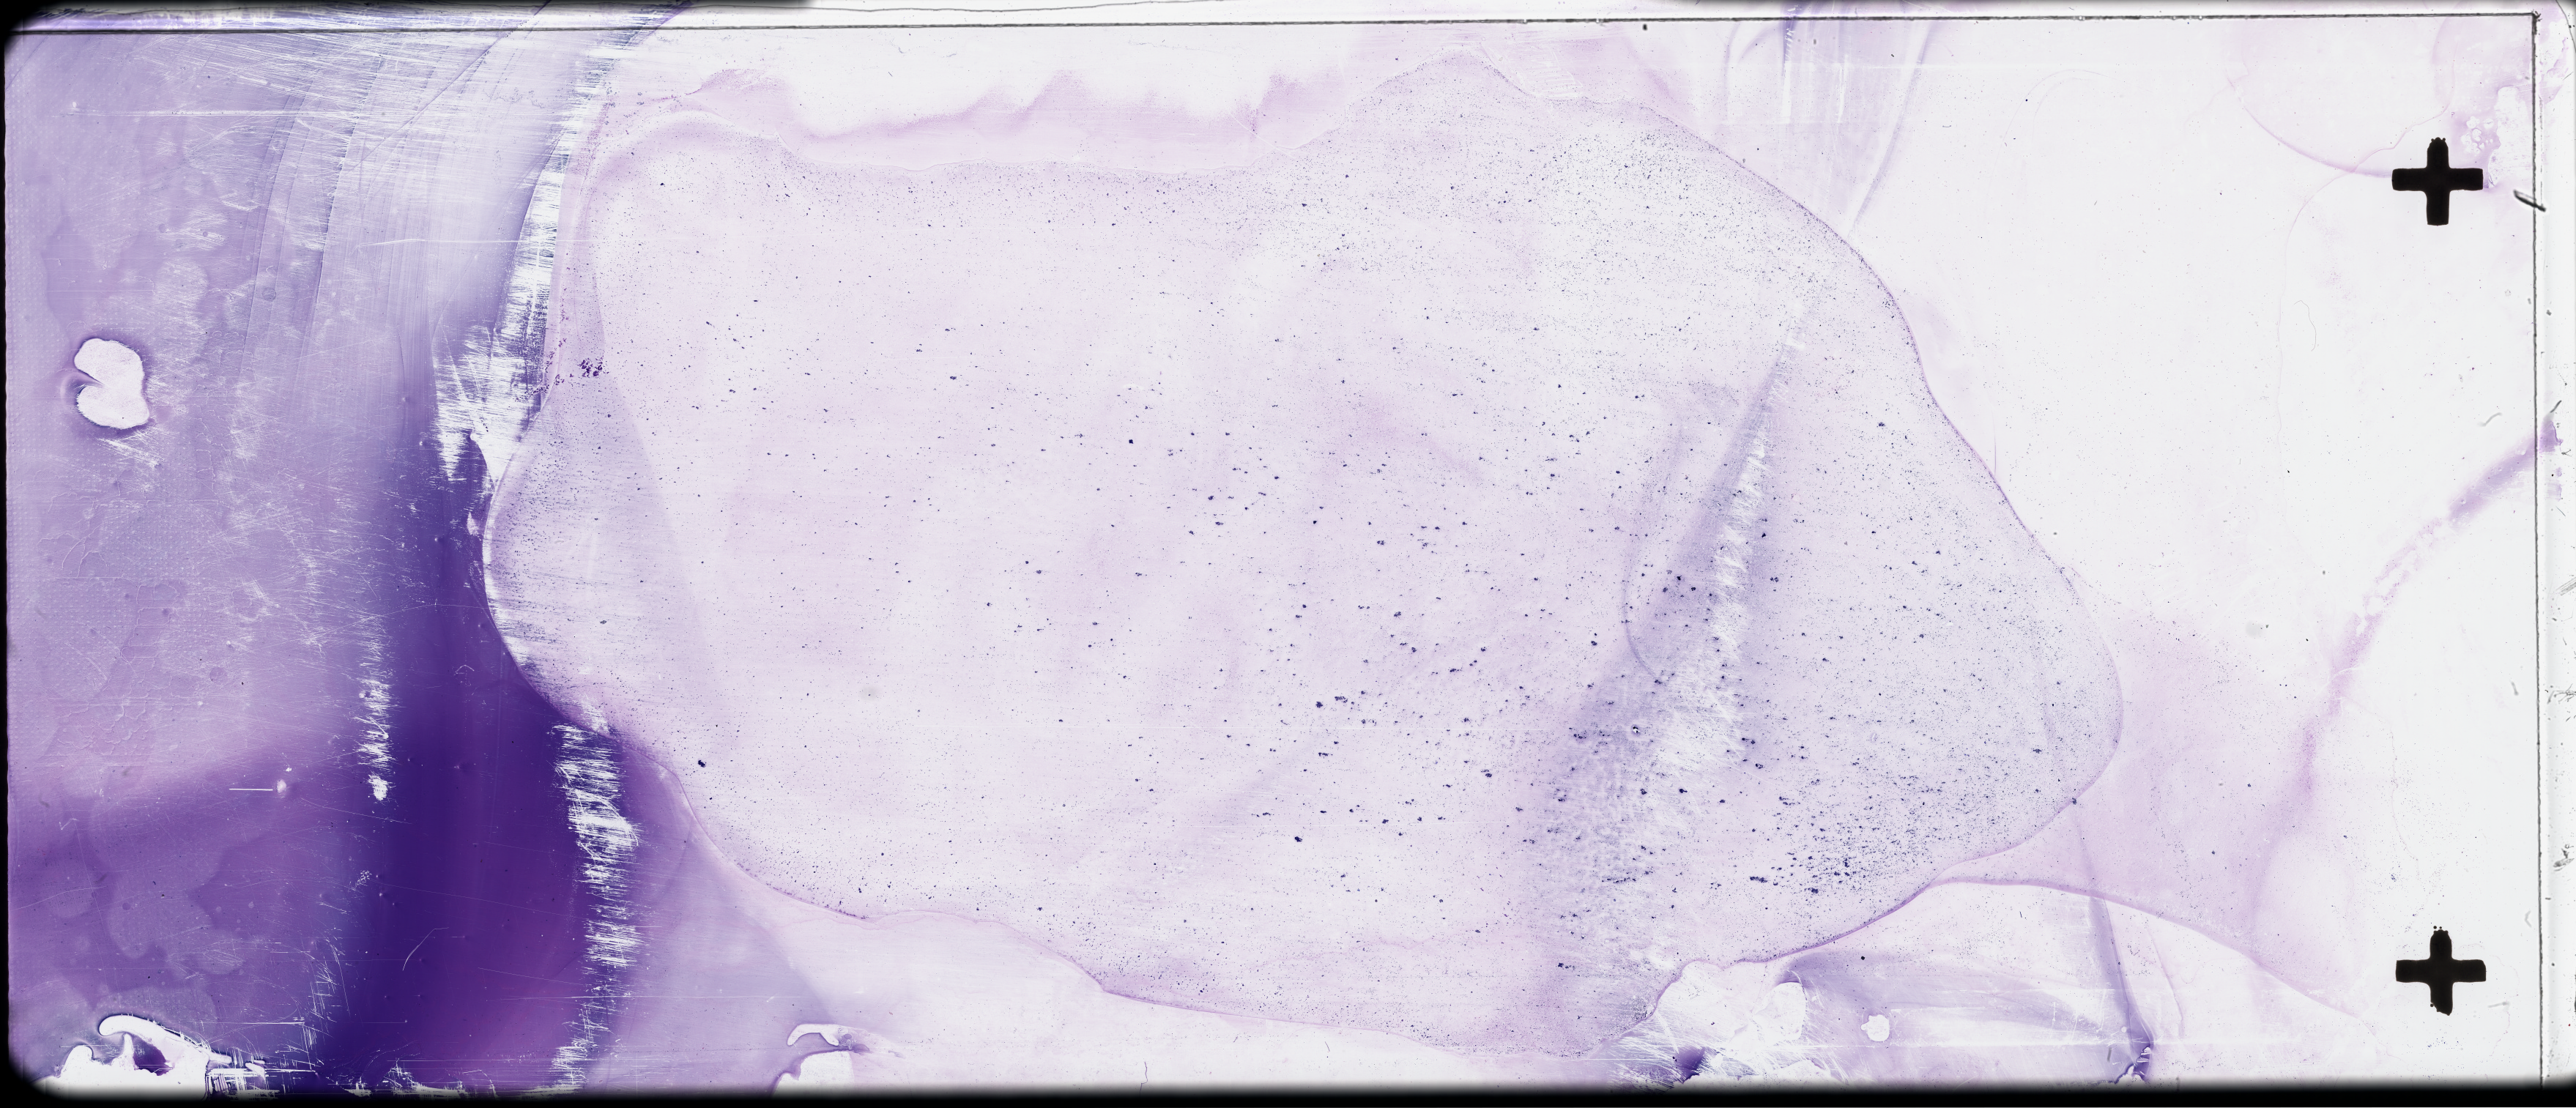
H&E-stained whole-slide image — whole scanned area (about 56.8 x 24.4 mm) shown as a low-resolution overview. Bone marrow (leukaemic) sample. Patient: female, age 38 years. Blasts: 80%.
FAB classification: M0. Diagnosis: Acute Myeloid Leukemia.